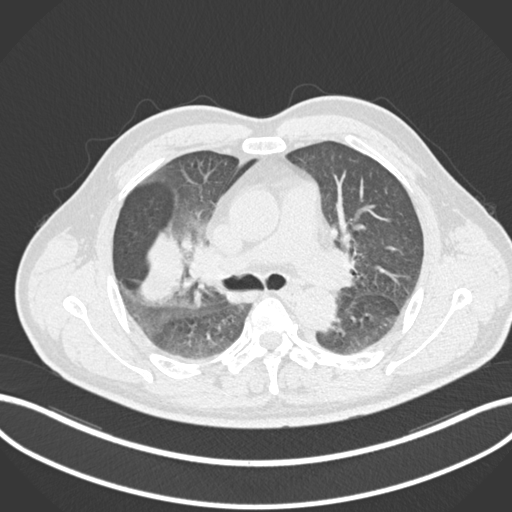
Chest CT, one axial slice. Slice 644 of 852 in the series (ordered by position). 120 kVp. Lung window (W 1500 / L -600 HU). 1 mm slice thickness. 512 × 512 image matrix, field of view 400 × 400 mm. Male patient, age 55 years. Case-level facts recorded for this patient, not image findings: clinical TNM (as recorded): T3 N2 M1.
Annotated regions visible in this slice (rectangle marked by the reading radiologist):
- lung tumour (recorded histology: adenocarcinoma): box from (x=137, y=223) to (x=185, y=306) px